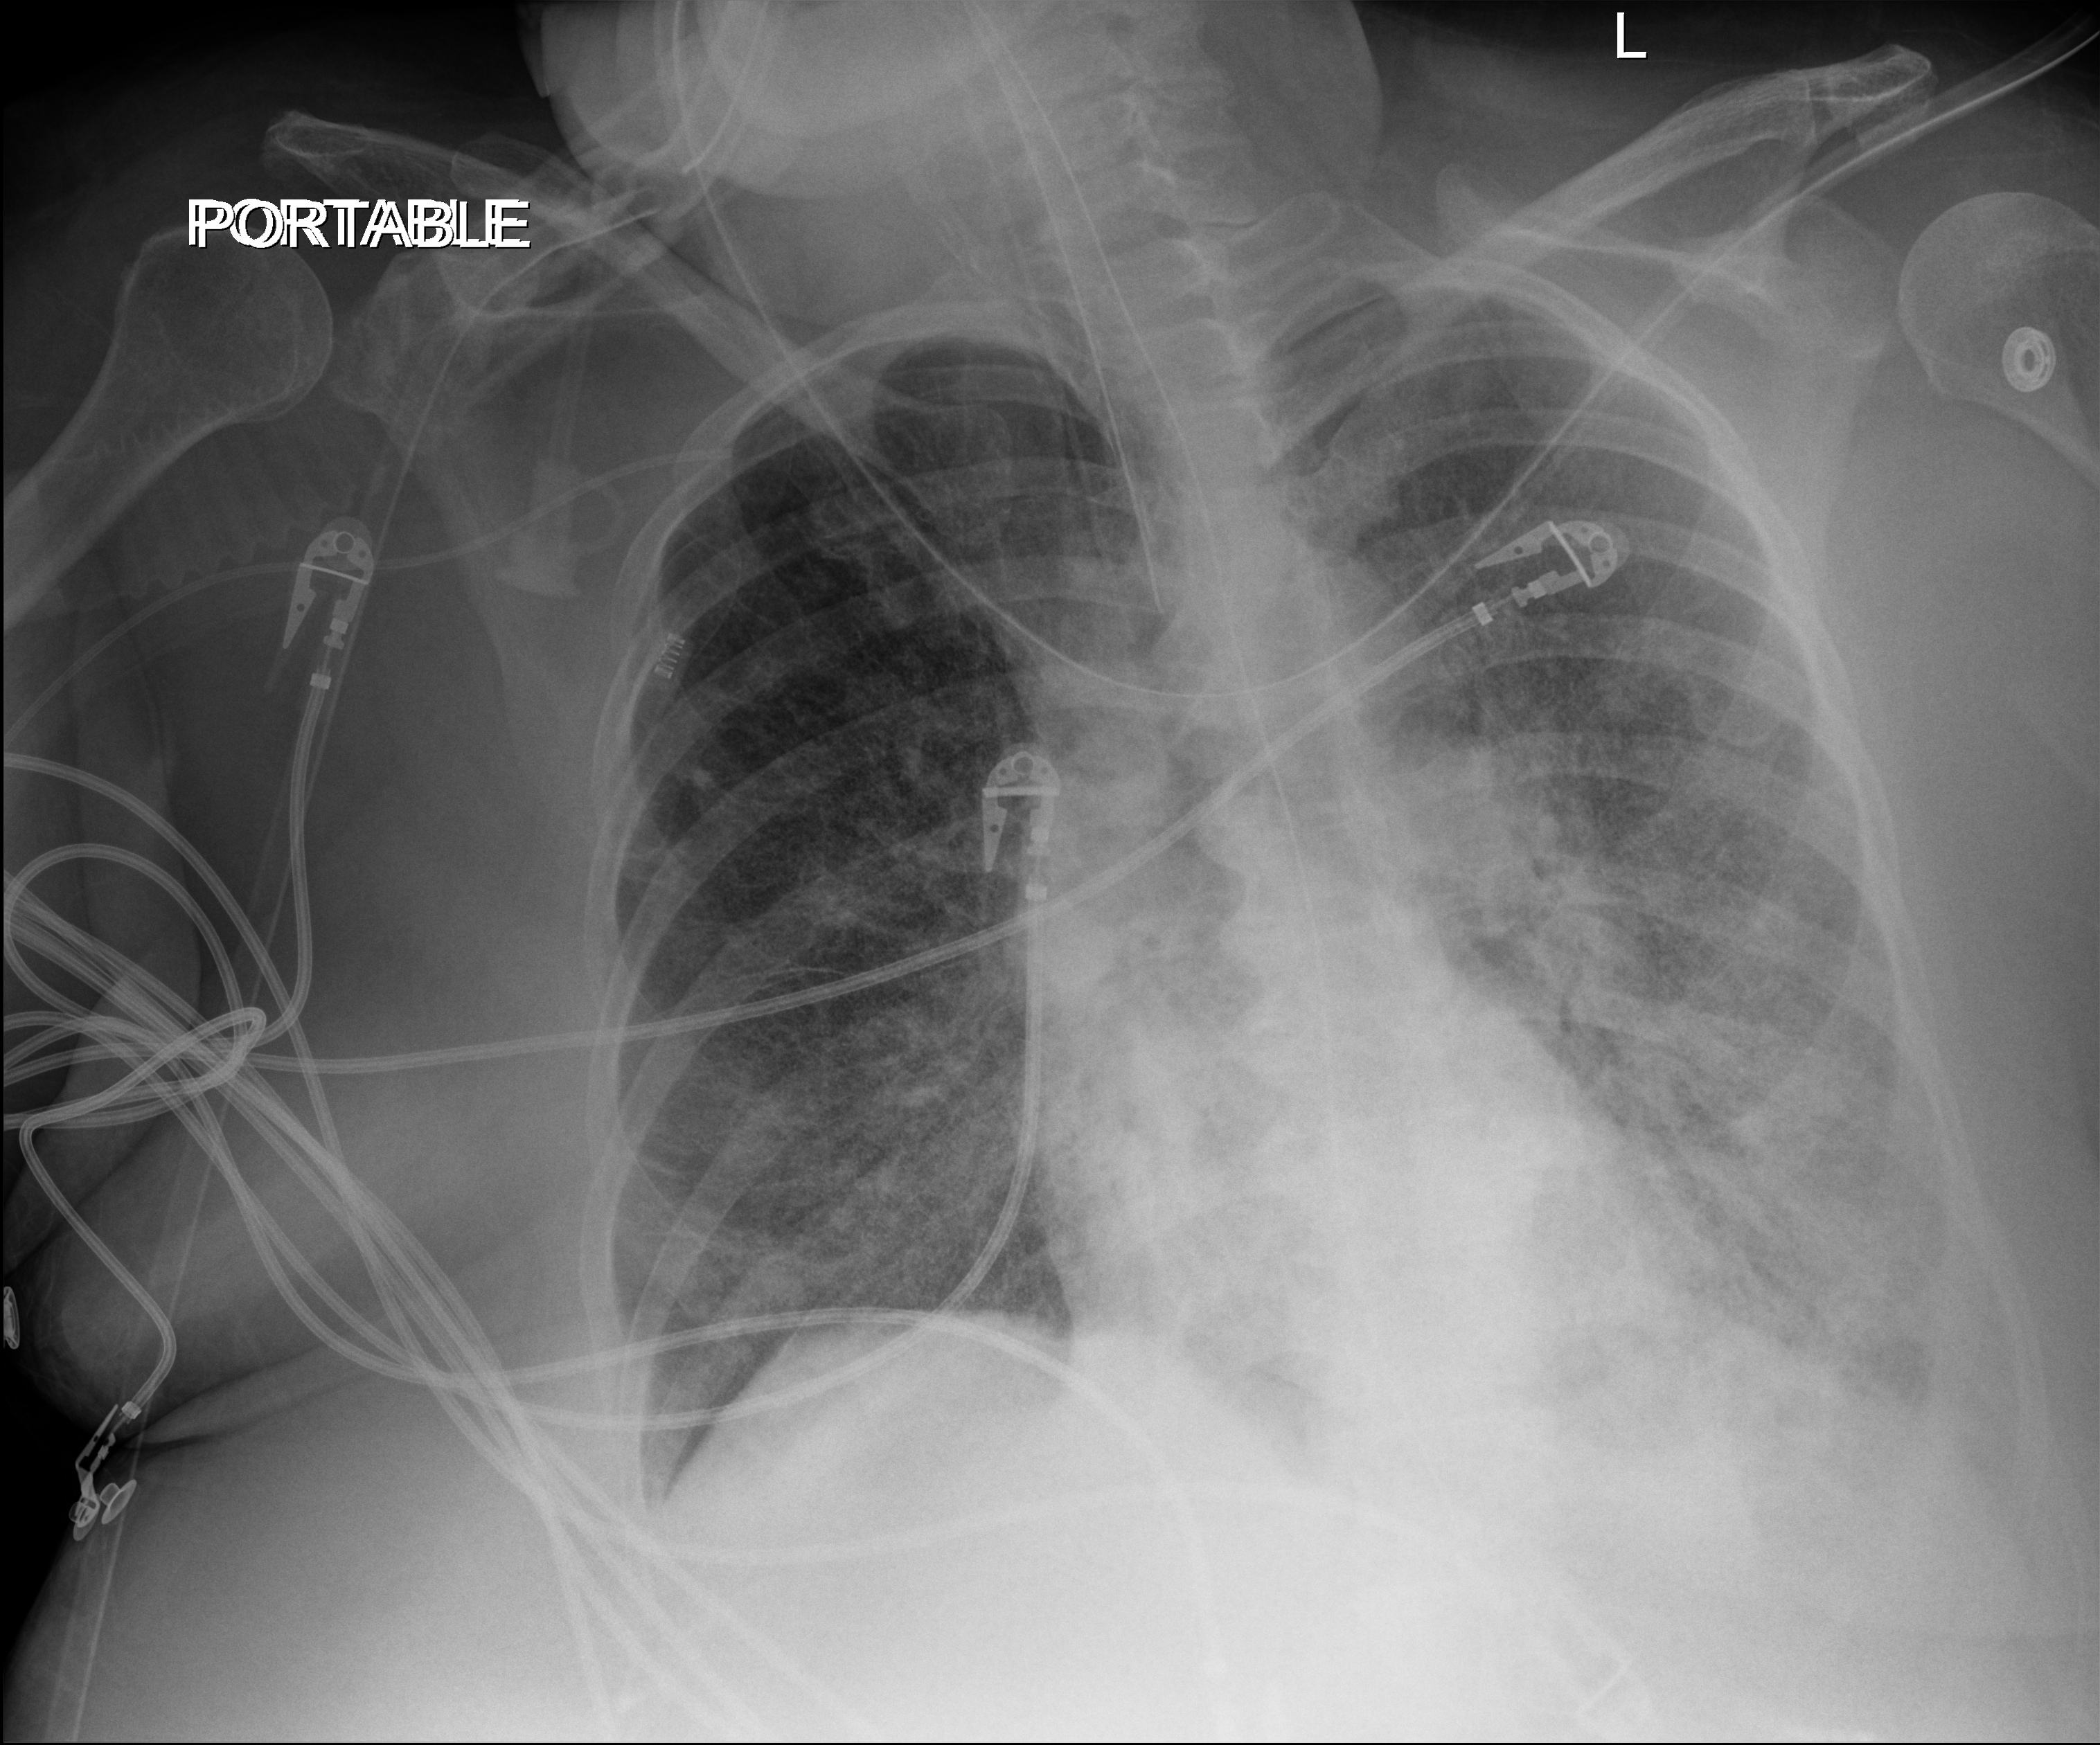
Bedside chest radiograph (digital radiography), anteroposterior (AP) projection. Patient hospitalised with COVID-19; female, aged 60–74 years.
Hospital-stay facts (about this admission, not read from this image; timing relative to this image not recorded): COPD (admission record): no; mechanically ventilated during this hospital stay: yes; length of hospital stay: 38 days.